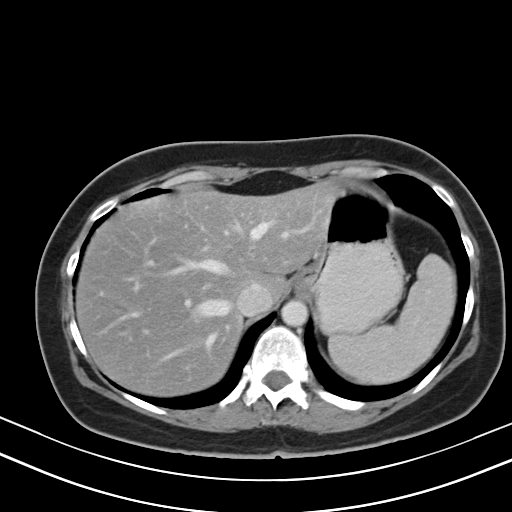
Contrast-enhanced abdominal CT, one axial slice. Slice 38 of 47 in the series (ordered by position). 130 kVp. Intravenous contrast given. Soft-tissue window (W 400 / L 40 HU). 512 × 512 image matrix, field of view 350 × 350 mm. Female patient. Case-level facts recorded for this patient, not image findings: diagnosis: colorectal cancer liver metastases, imaged before liver resection; multiple liver metastases: no.
Structures marked on this image (manually delineated by an expert):
- hepatic veins: bounding box <100,222,308,359> (left, top, right, bottom; pixels)
- liver: <76,188,330,396>
- planned liver remnant (the part of the liver to remain after resection): <76,188,330,396>
- portal vein (with intrahepatic branches): <129,231,289,340>